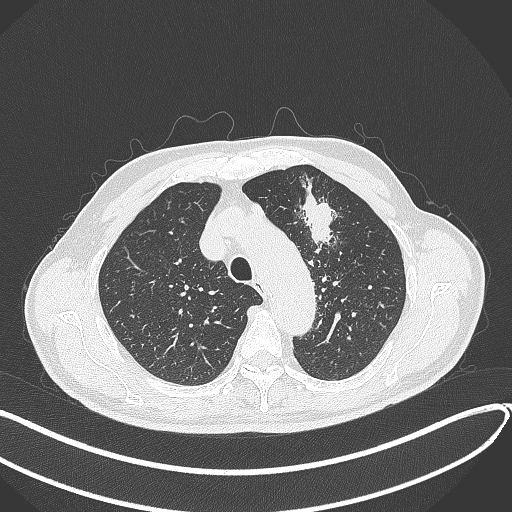
Chest CT, one axial slice; slice 320 of 459 in the series (ordered by position); reconstruction kernel B70f; lung window (W 1500 / L -600 HU); 512 × 512 image matrix. Male patient, age 74 years. From the clinical record (not read from this slice): clinical TNM (as recorded): T2b N0 M1c.
Annotated regions visible in this slice (rectangle marked by the reading radiologist):
- lung tumour (recorded histology: adenocarcinoma): box from (x=298, y=175) to (x=344, y=249) px